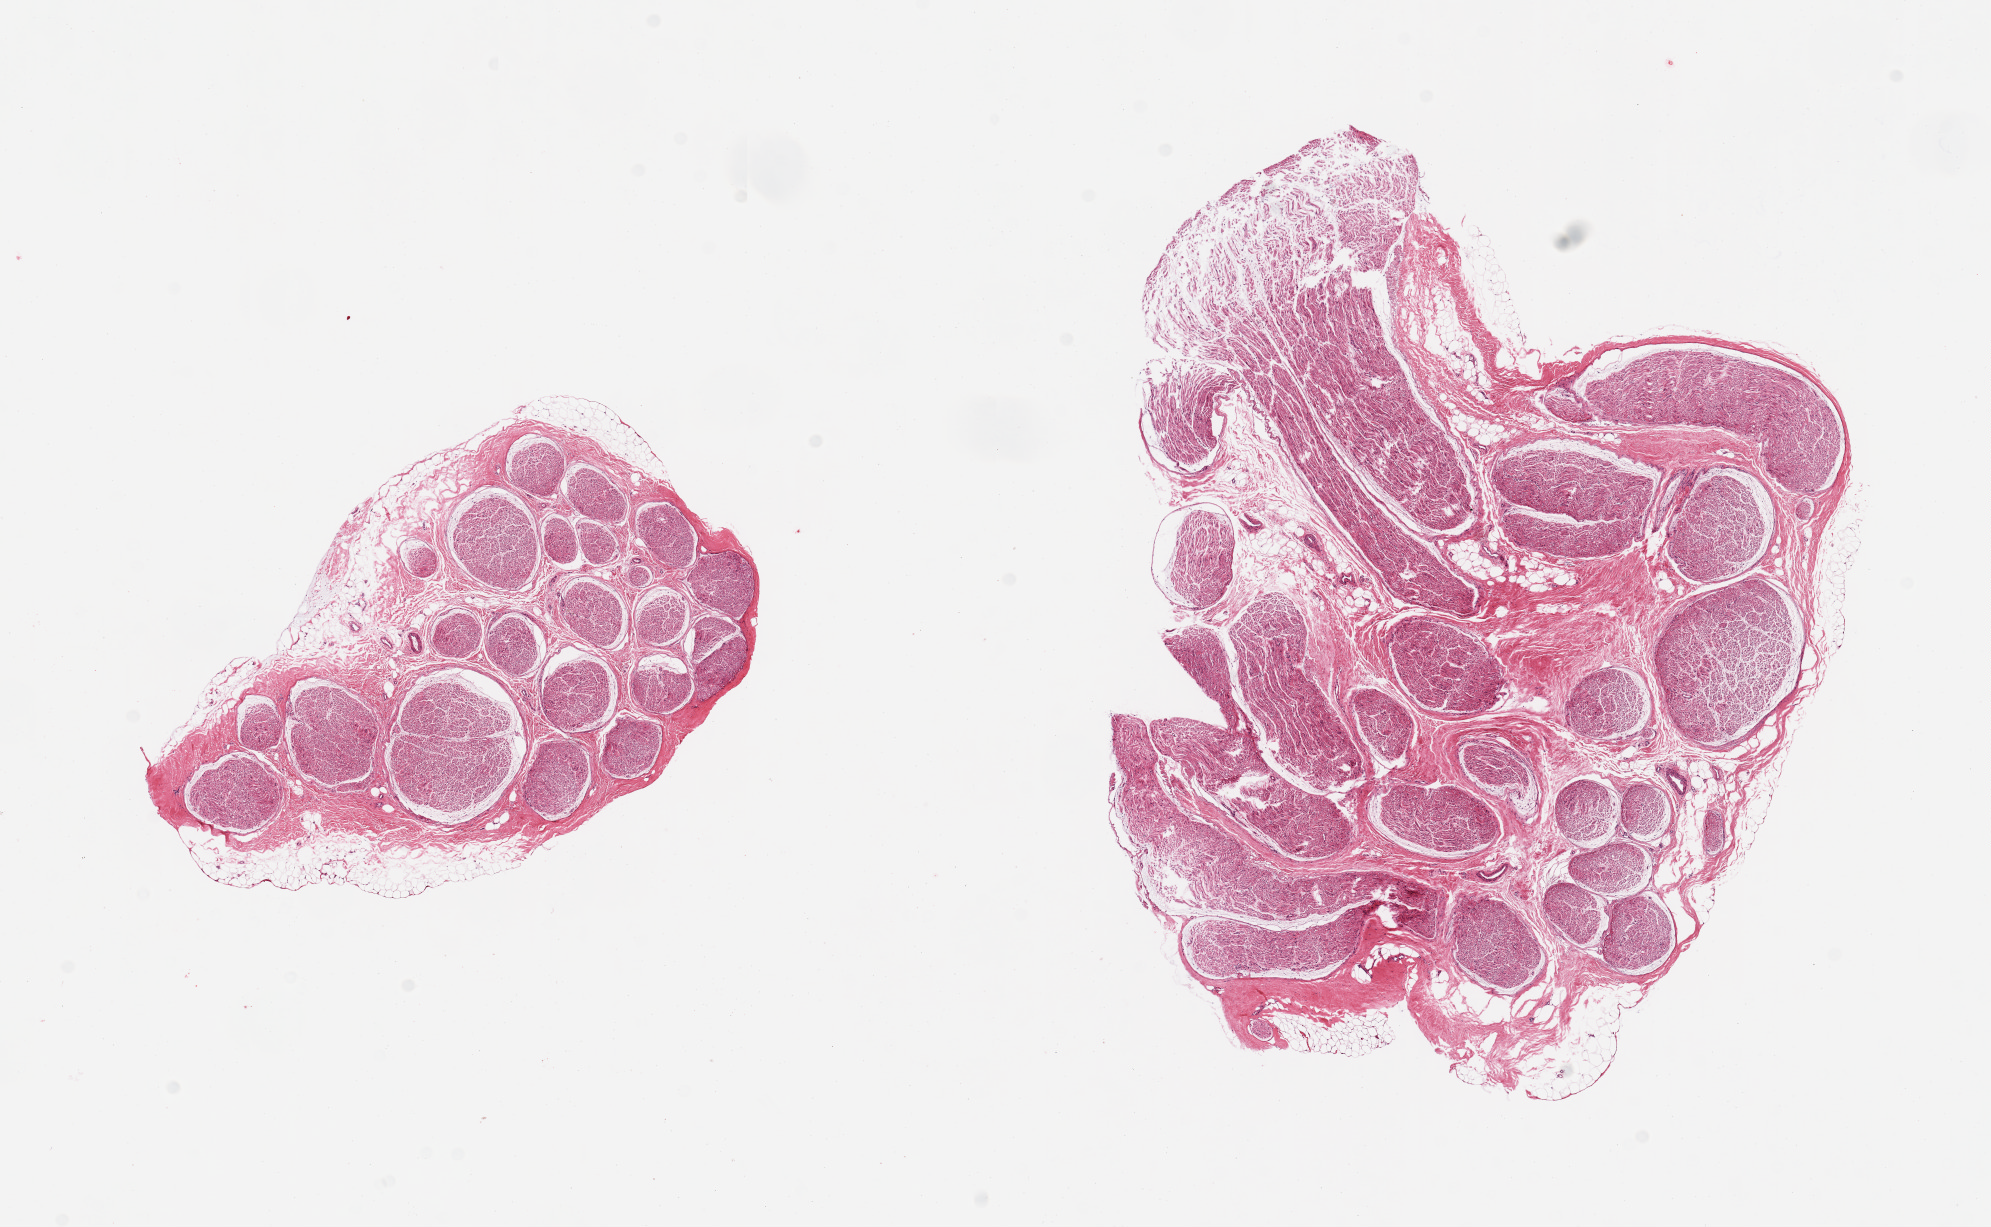
Hematoxylin and eosin (H&E) whole-slide image — low-resolution overview of the scanned area, about 15.8 x 9.7 mm (slide scanned at 20x). PAXgene-fixed paraffin-embedded (PFPE) section. Sampled site (target tissue): tibial nerve. Tissue donor sample.
* reviewer comment on this tissue sample: 2 pieces; 10% internal & external fat